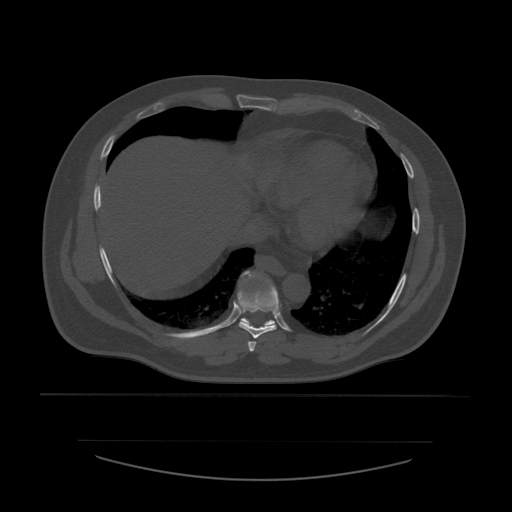
CT including the spine, one axial slice; position 332 of 532 along the scan axis; reconstruction kernel STANDARD; 120 kVp; bone window (W 1800 / L 400 HU); 1.25 mm slice thickness; 512 × 512 image matrix, field of view 441 × 441 mm. Patient age 44 years. From the clinical record (not read from this slice): primary cancer: soft tissue sarcoma.
Outlined on this slice (semi-automatically segmented with operator editing):
- T7 vertebra: box from (x=248, y=341) to (x=257, y=353) px
- T8 vertebra: (x=236, y=286)–(x=279, y=339)
- T9 vertebra: (x=240, y=271)–(x=278, y=328)